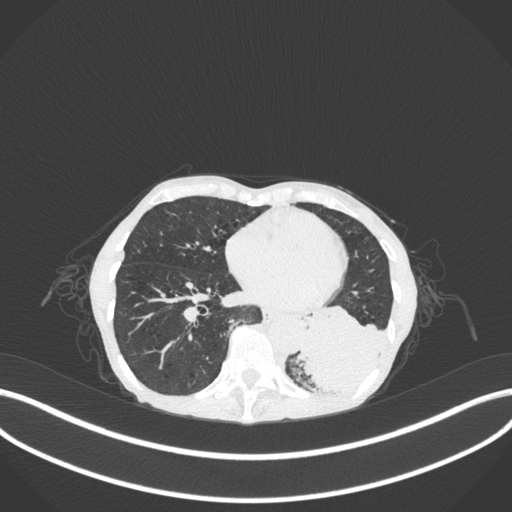
Chest CT, one axial slice. Slice 93 of 347 in the series (ordered by position). Lung window (W 1500 / L -600 HU). 512 × 512 image matrix, field of view 400 × 400 mm. Female patient, age 70 years. Case-level facts recorded for this patient, not image findings: clinical TNM (as recorded): T3 N0 M0.
Structures marked on this image (rectangle marked by the reading radiologist):
- lung tumour (recorded histology: small cell carcinoma): bounding box [x1, y1, x2, y2] px = [296, 300, 396, 397]